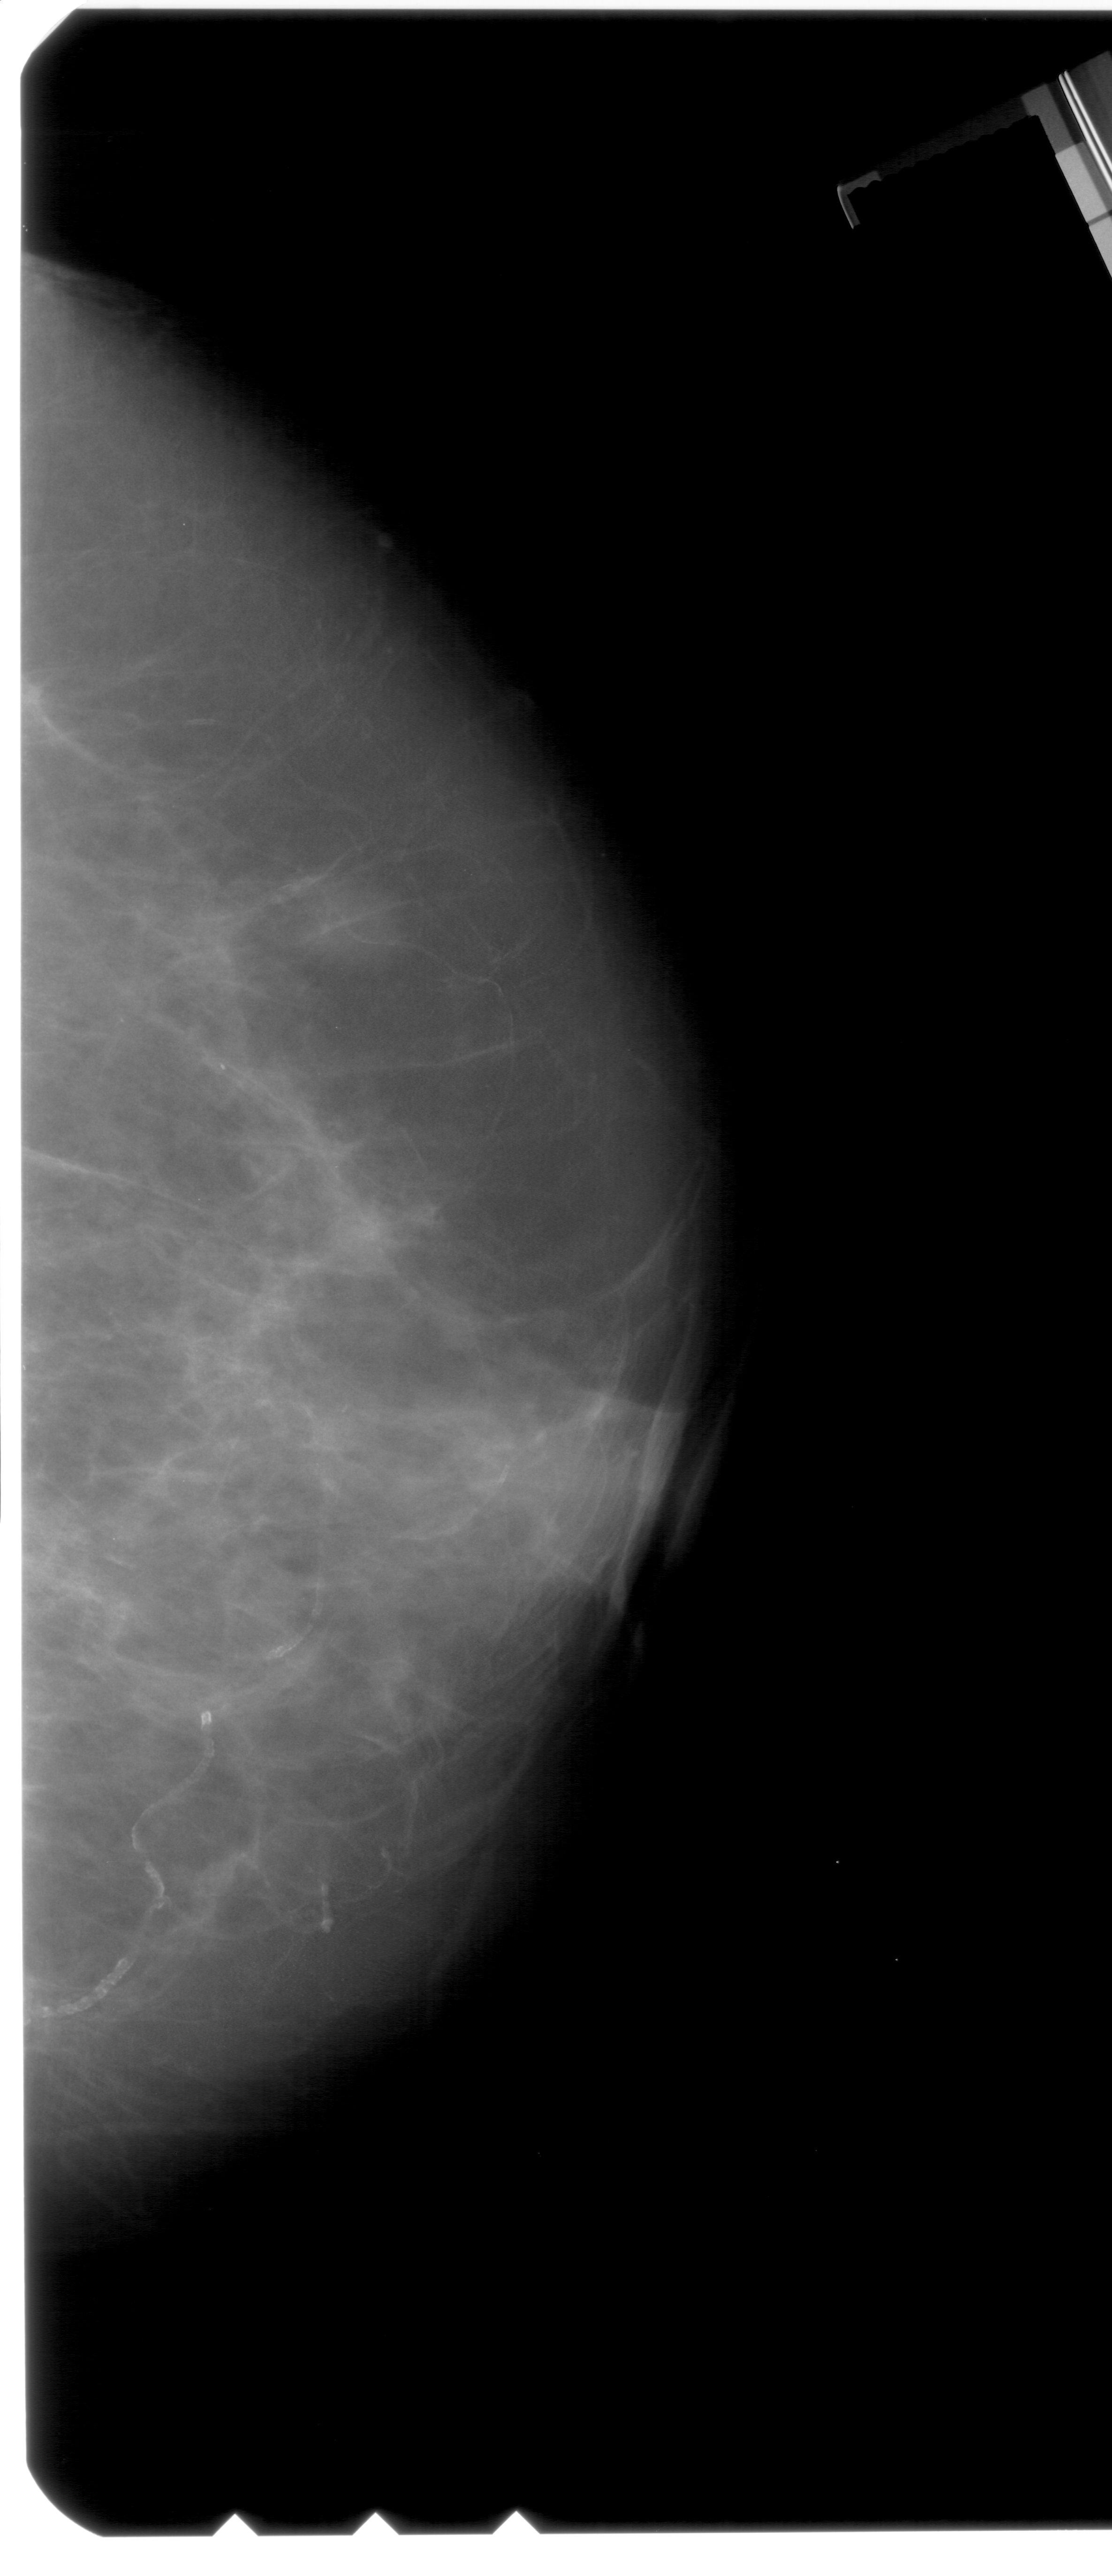
Scanned film-screen mammogram; right breast; CC view.
- Finding: mass, shape oval, margins ill defined; BI-RADS assessment category 4; pathology result (as recorded, not read from the image): benign.